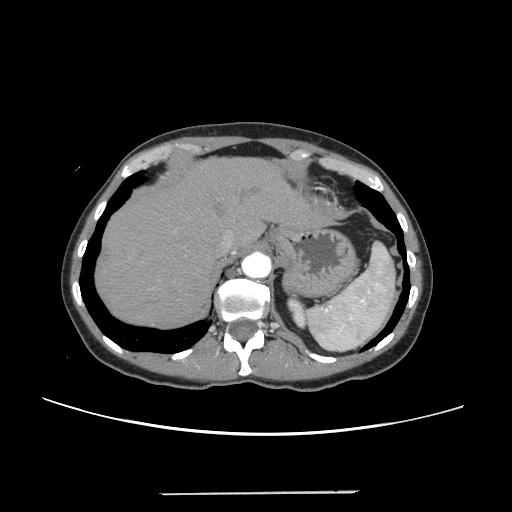
Contrast-enhanced abdominal CT, one axial slice; 120 kVp; intravenous contrast given; soft-tissue window (W 400 / L 40 HU); 1.25 mm slice thickness; 512 × 512 image matrix, field of view 371 × 371 mm. Female patient, age 60 years. From the clinical record (not read from this slice): diagnosis: colorectal cancer liver metastases, imaged before liver resection; multiple liver metastases: no; largest metastasis: 1.5 cm; chemotherapy before resection: yes.
Structures marked on this image (expert manual segmentation):
- hepatic veins: bounding box (x1, y1, x2, y2) in pixels: (217, 218, 249, 252)
- liver: (96, 158, 325, 327)
- planned liver remnant (the part of the liver to remain after resection): (96, 158, 324, 327)